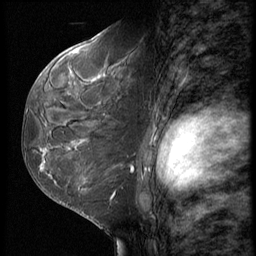
Breast MRI (dynamic contrast-enhanced), one sagittal slice; position 36 of 62 along the scan axis; 3 images stored at this slice position (order not interpretable as contrast timing); 1.5 T; TE 4.2 ms, TR 9 ms; 2.5 mm slice thickness; 256 × 256 image matrix, field of view 180 × 180 mm. Female patient, age 50 years. From the clinical record (not read from this slice): setting: breast cancer imaged before/during neoadjuvant chemotherapy; receptor status: HR-positive, HER2-negative.
Outlined on this slice (semi-automatically segmented with operator editing):
- analysis volume of interest (the breast-tissue region the enhancement analysis was run in; not a lesion): box from (x=32, y=91) to (x=118, y=209) px
- tumour enhancement mask (voxels above the 140 % enhancement threshold inside the analysis volume of interest): (x=41, y=140)–(x=113, y=199)